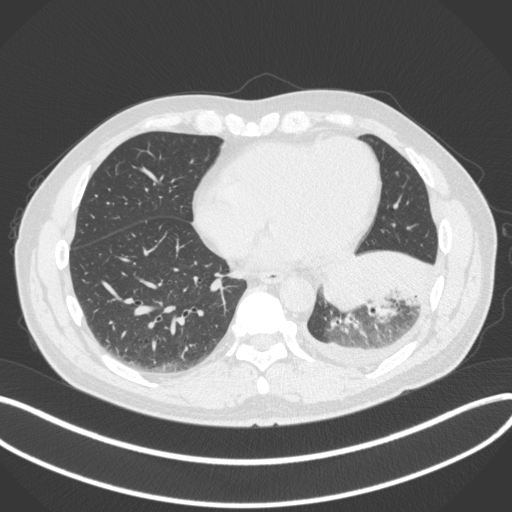
Chest CT, one axial slice. Slice 119 of 350 in the series (ordered by position). Lung window (W 1500 / L -600 HU). 1 mm slice thickness. 512 × 512 image matrix, field of view 400 × 400 mm. Patient: male, 58 years. From the clinical record (not read from this slice): clinical TNM (as recorded): T3 N1 M1b; histopathological grade: G3.
Annotated regions visible in this slice (bounding box drawn by a radiologist):
- lung tumour (recorded histology: small cell carcinoma): bounding box <320,246,433,310> (left, top, right, bottom; pixels)